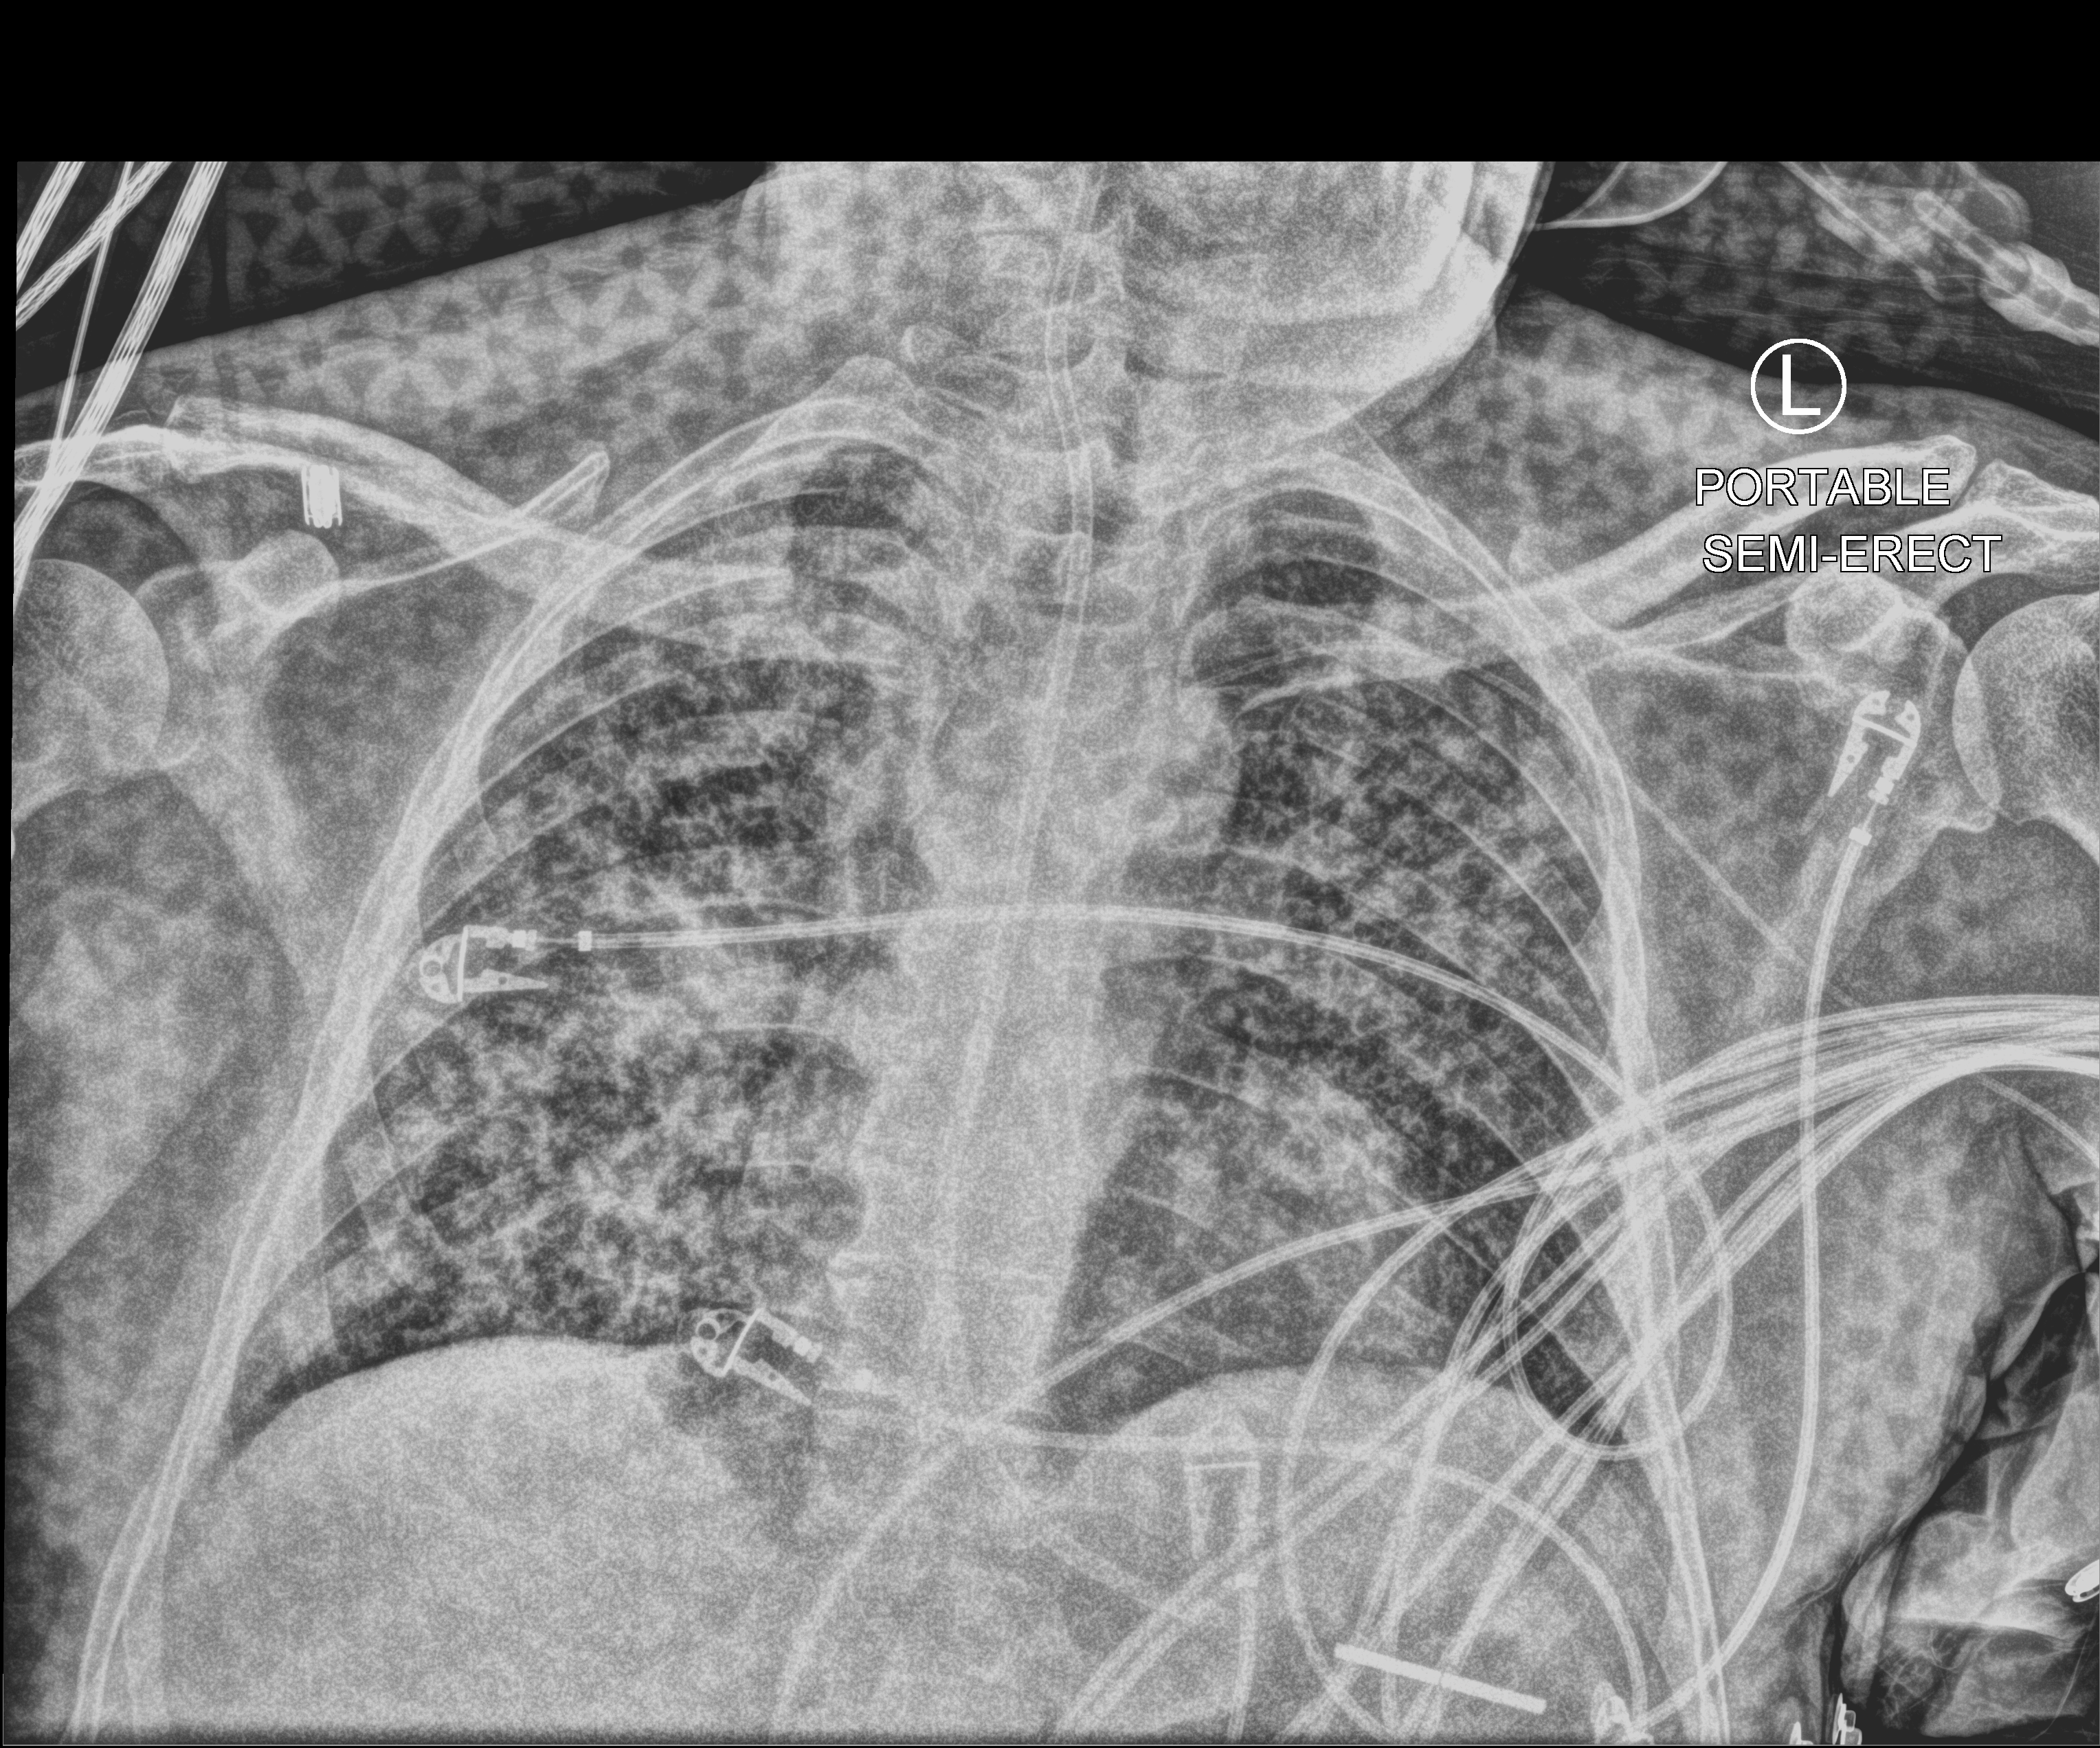
Chest X-ray (portable). Patient hospitalised with COVID-19; male, aged 18–59 years.
Hospital-stay facts (about this admission, not read from this image; timing relative to this image not recorded): diabetes (admission record): no.